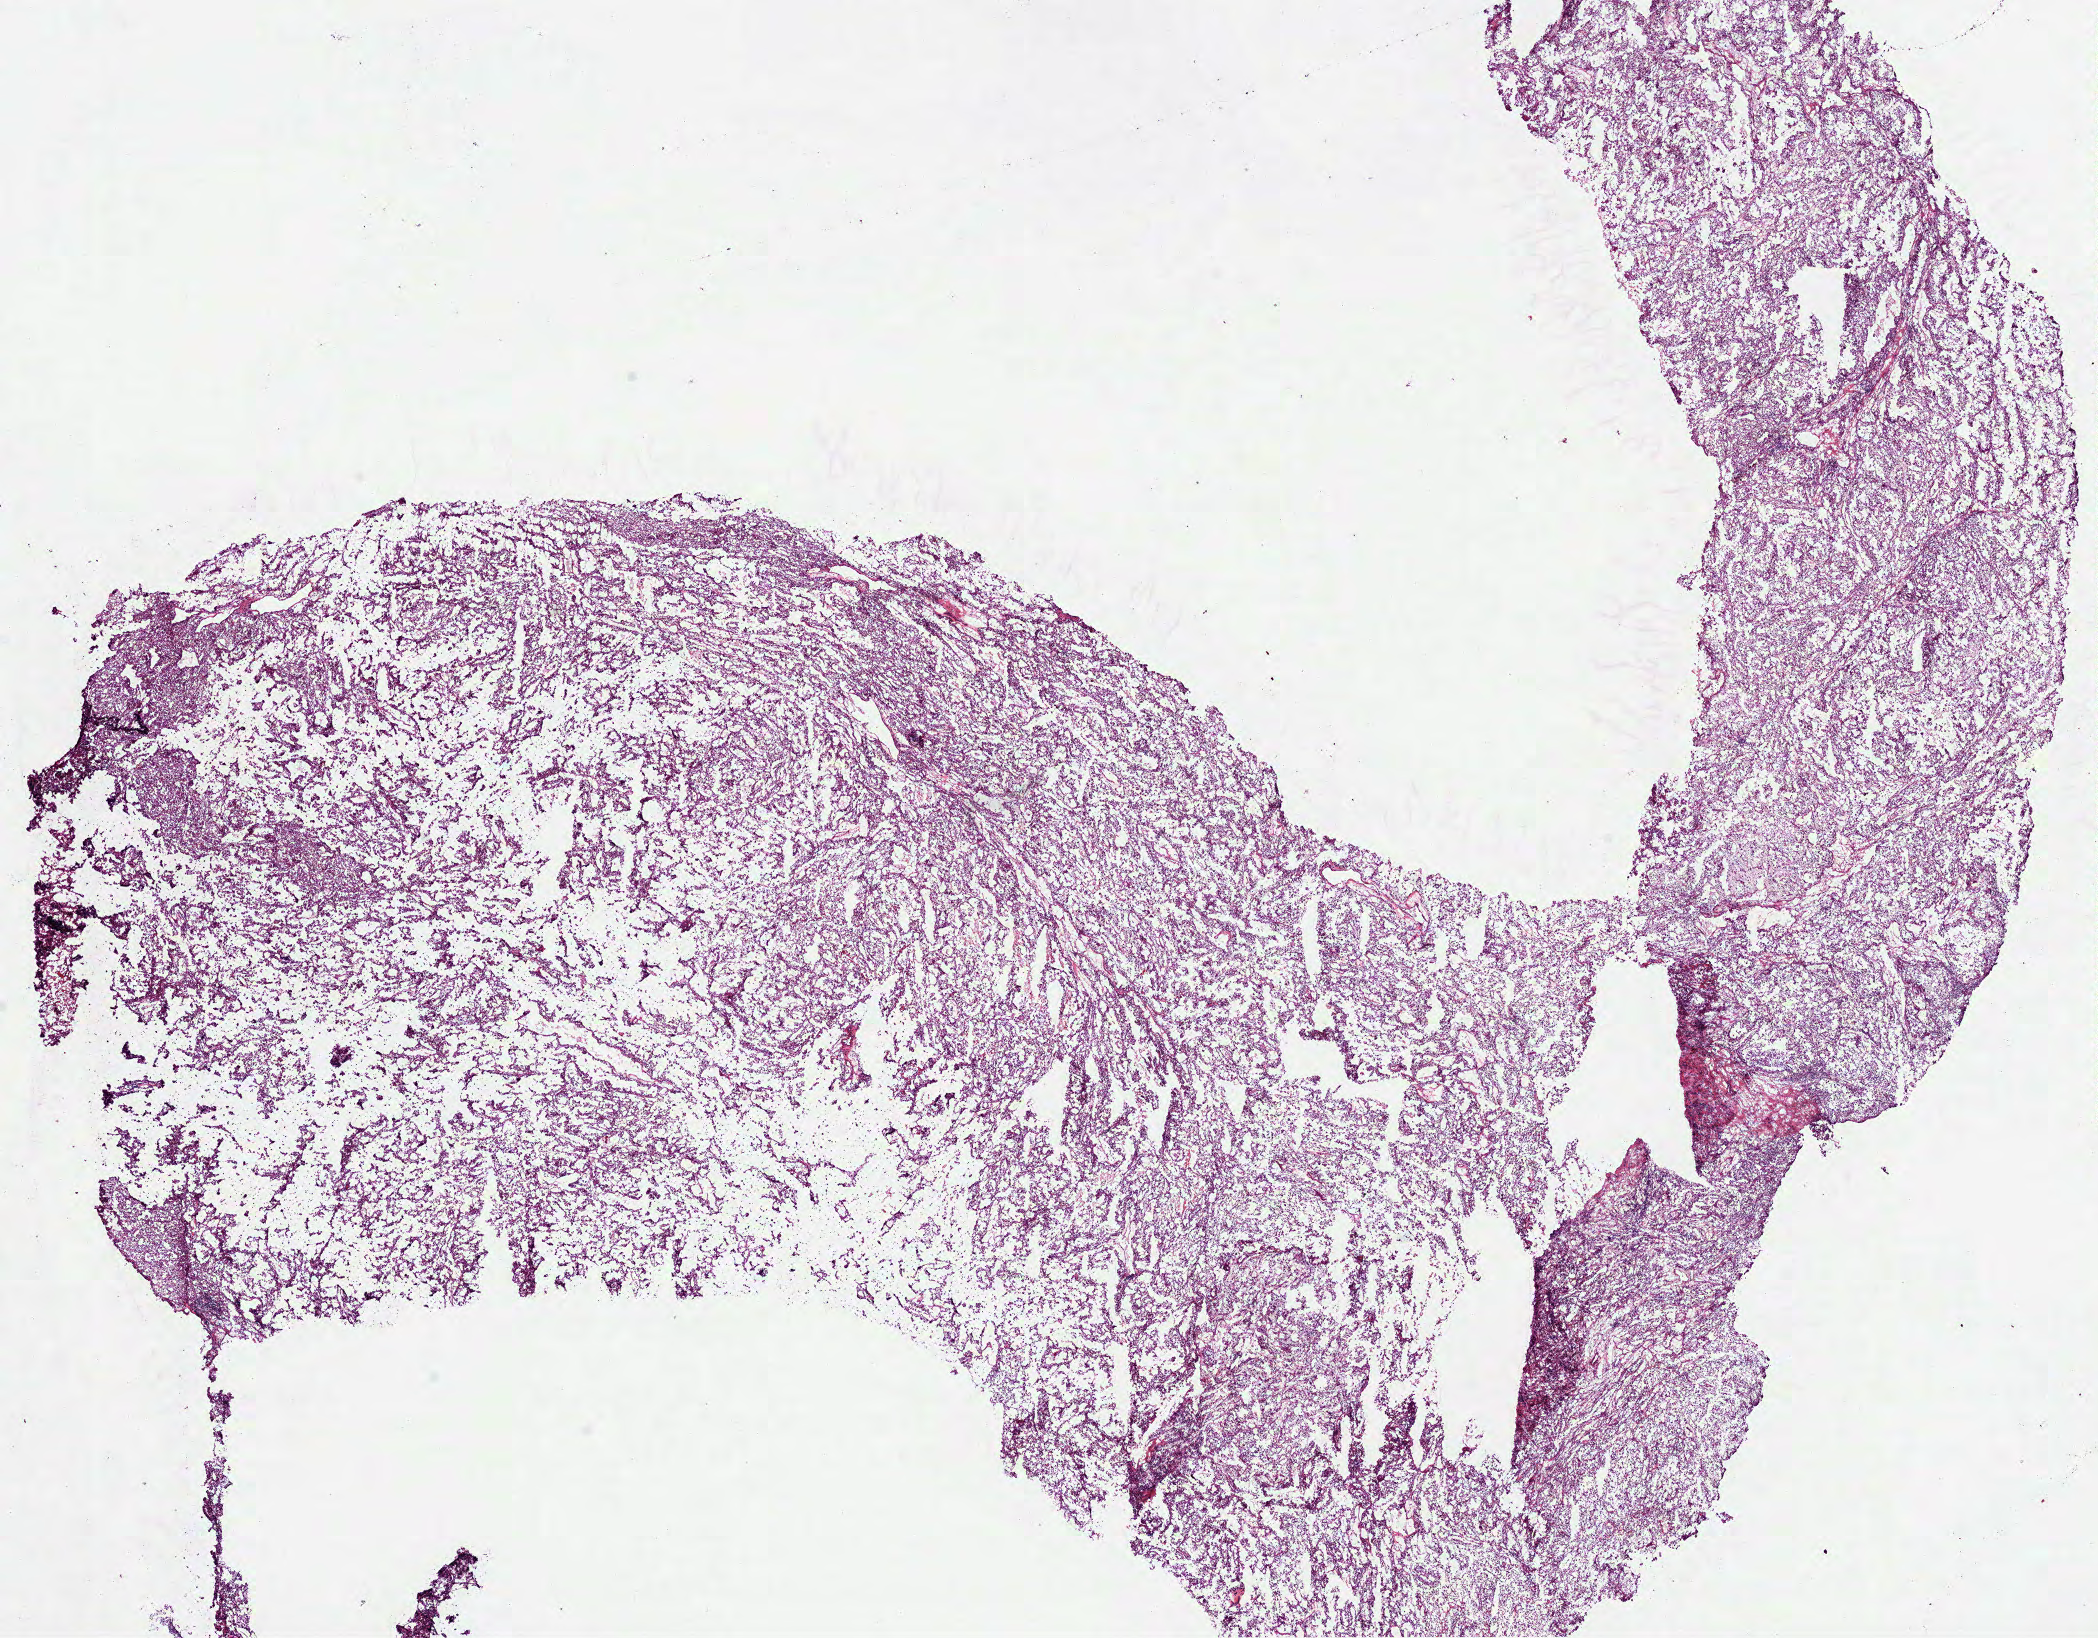
Whole-slide histology image, Hematoxylin and eosin (H&E) stained — whole scanned area (about 16.9 x 13.2 mm, slide scanned at 40x) shown as a low-resolution overview, frozen section, sample: primary tumour, kidney. Male, age 58 years at initial diagnosis.
Diagnosis: Clear cell adenocarcinoma, NOS.